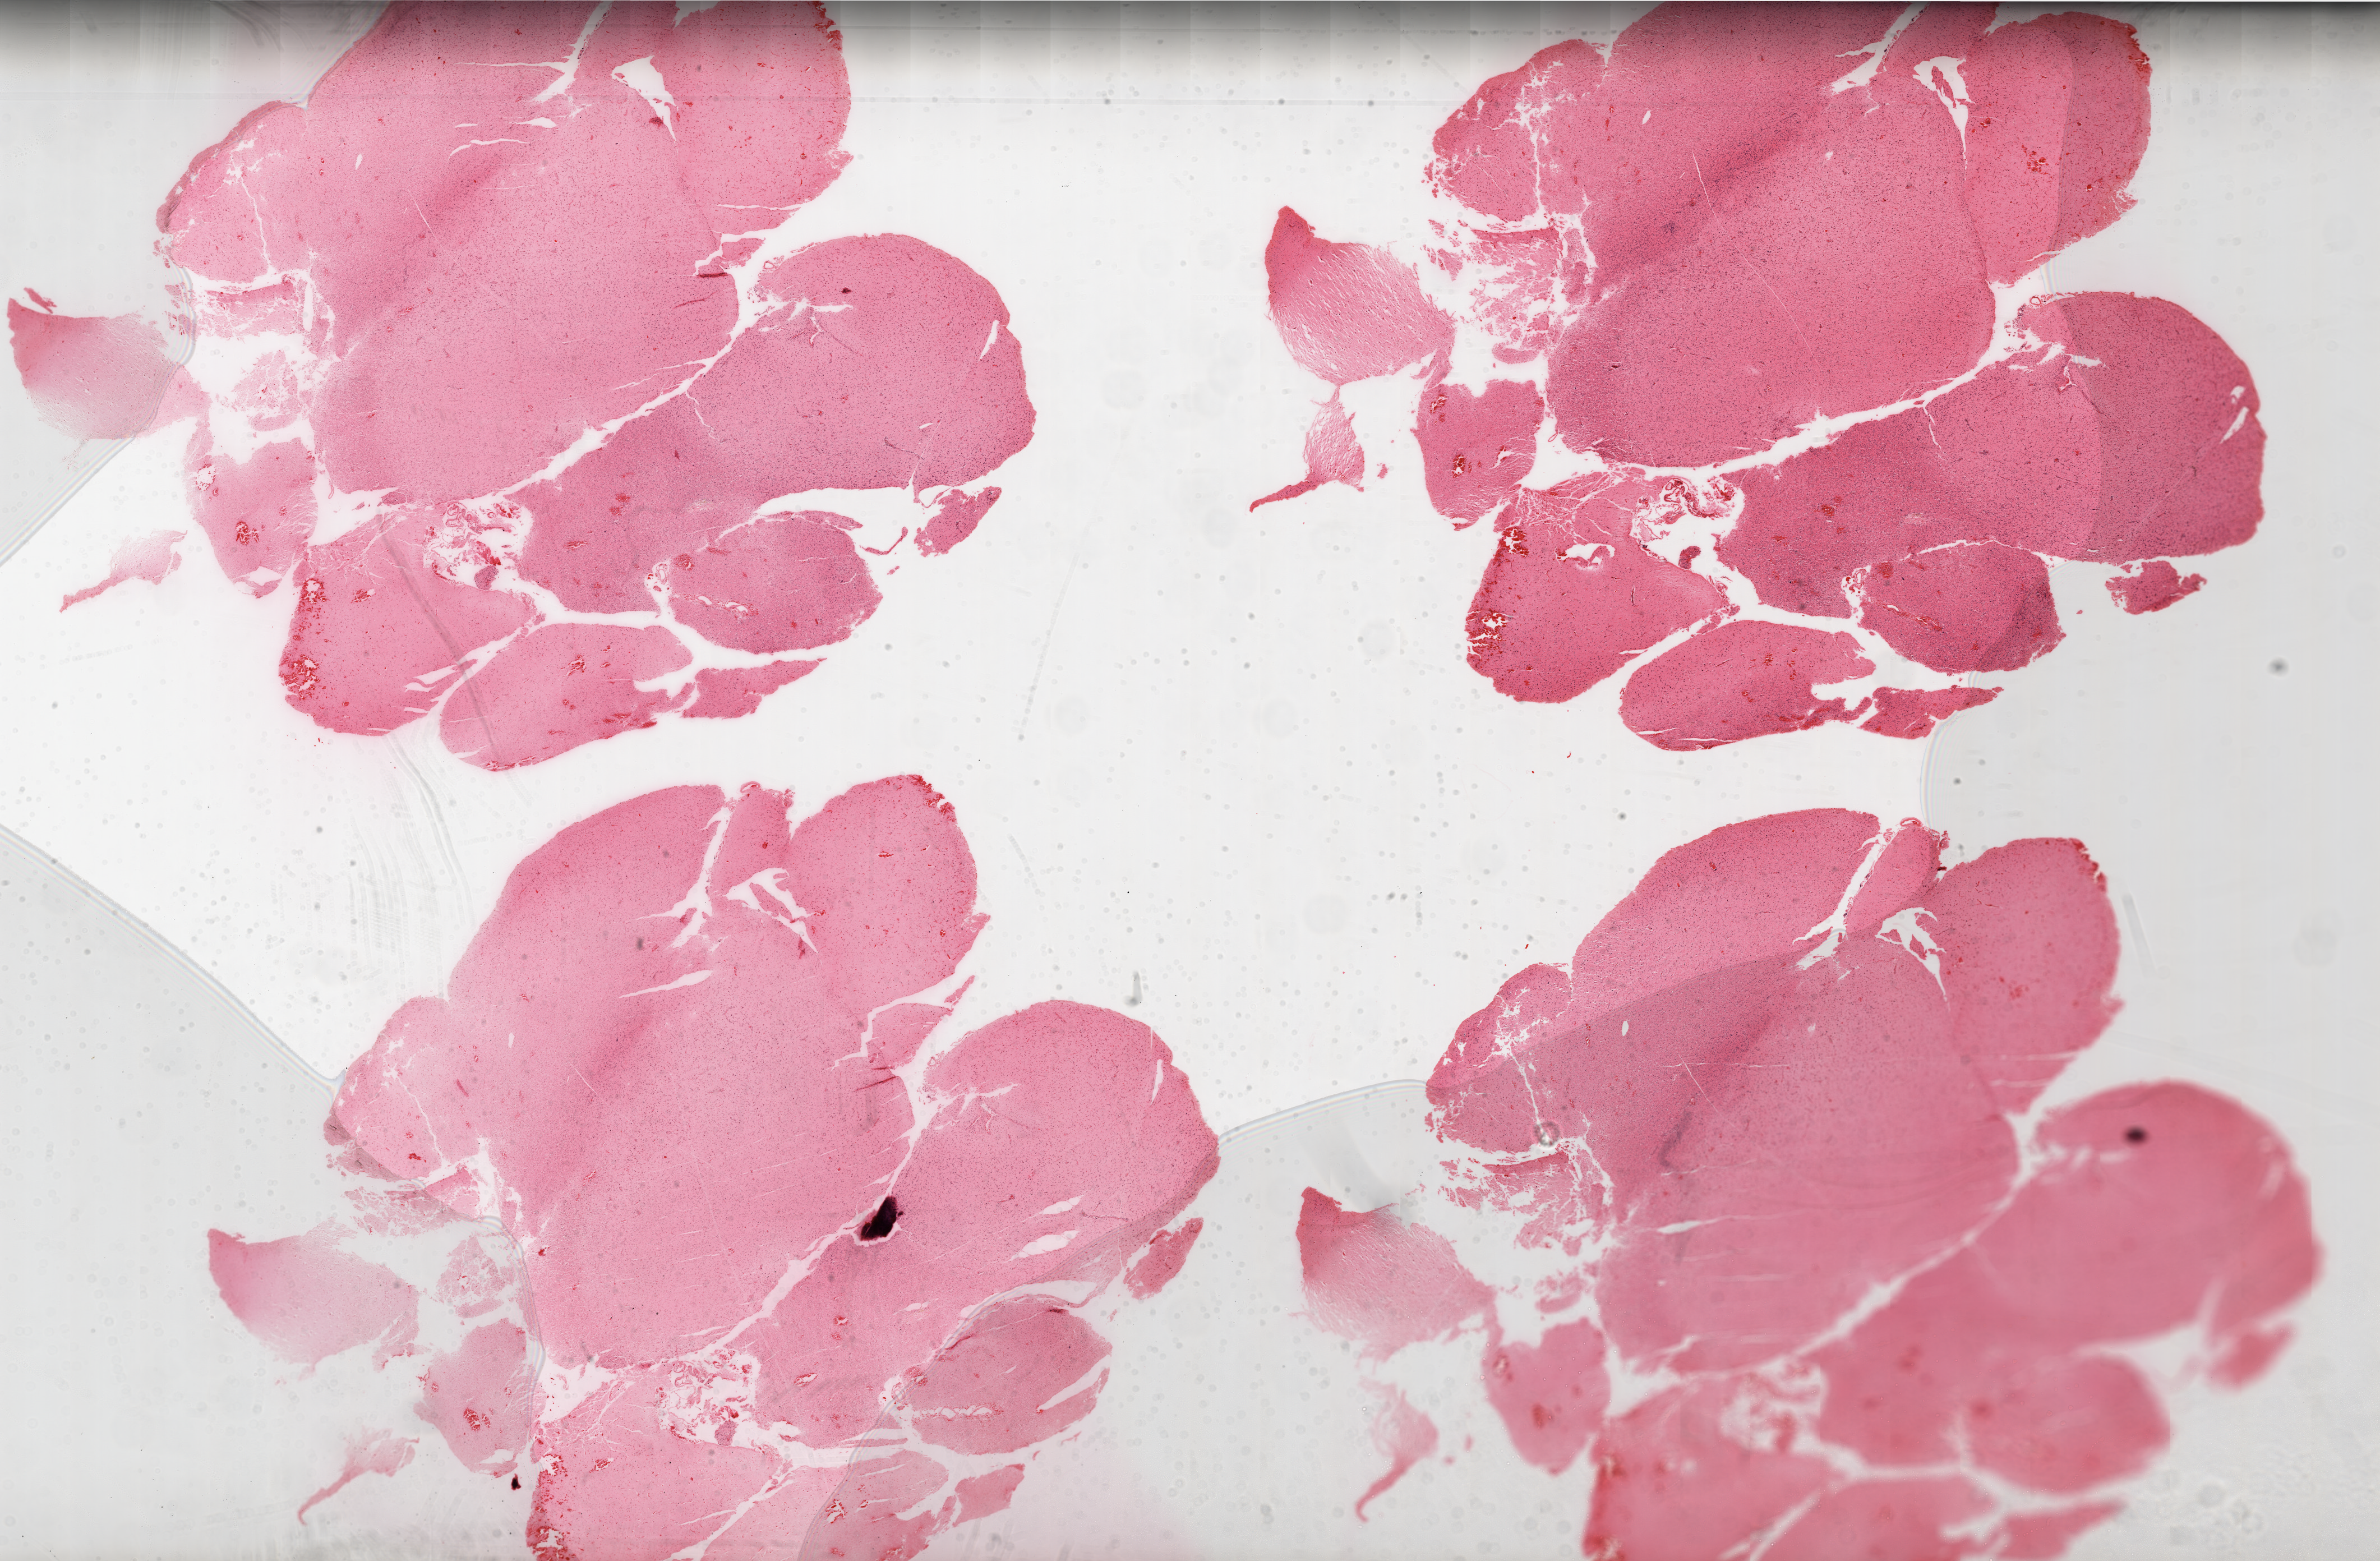
Whole-slide histology image, Hematoxylin and eosin (H&E) stained, a low-resolution overview of the entire scanned area, about 34.0 x 22.3 mm. Formalin-fixed paraffin-embedded (FFPE) diagnostic section. Sample: primary tumour, brain. Male patient; age at initial diagnosis 63 years.
• pathologic diagnosis: Glioblastoma